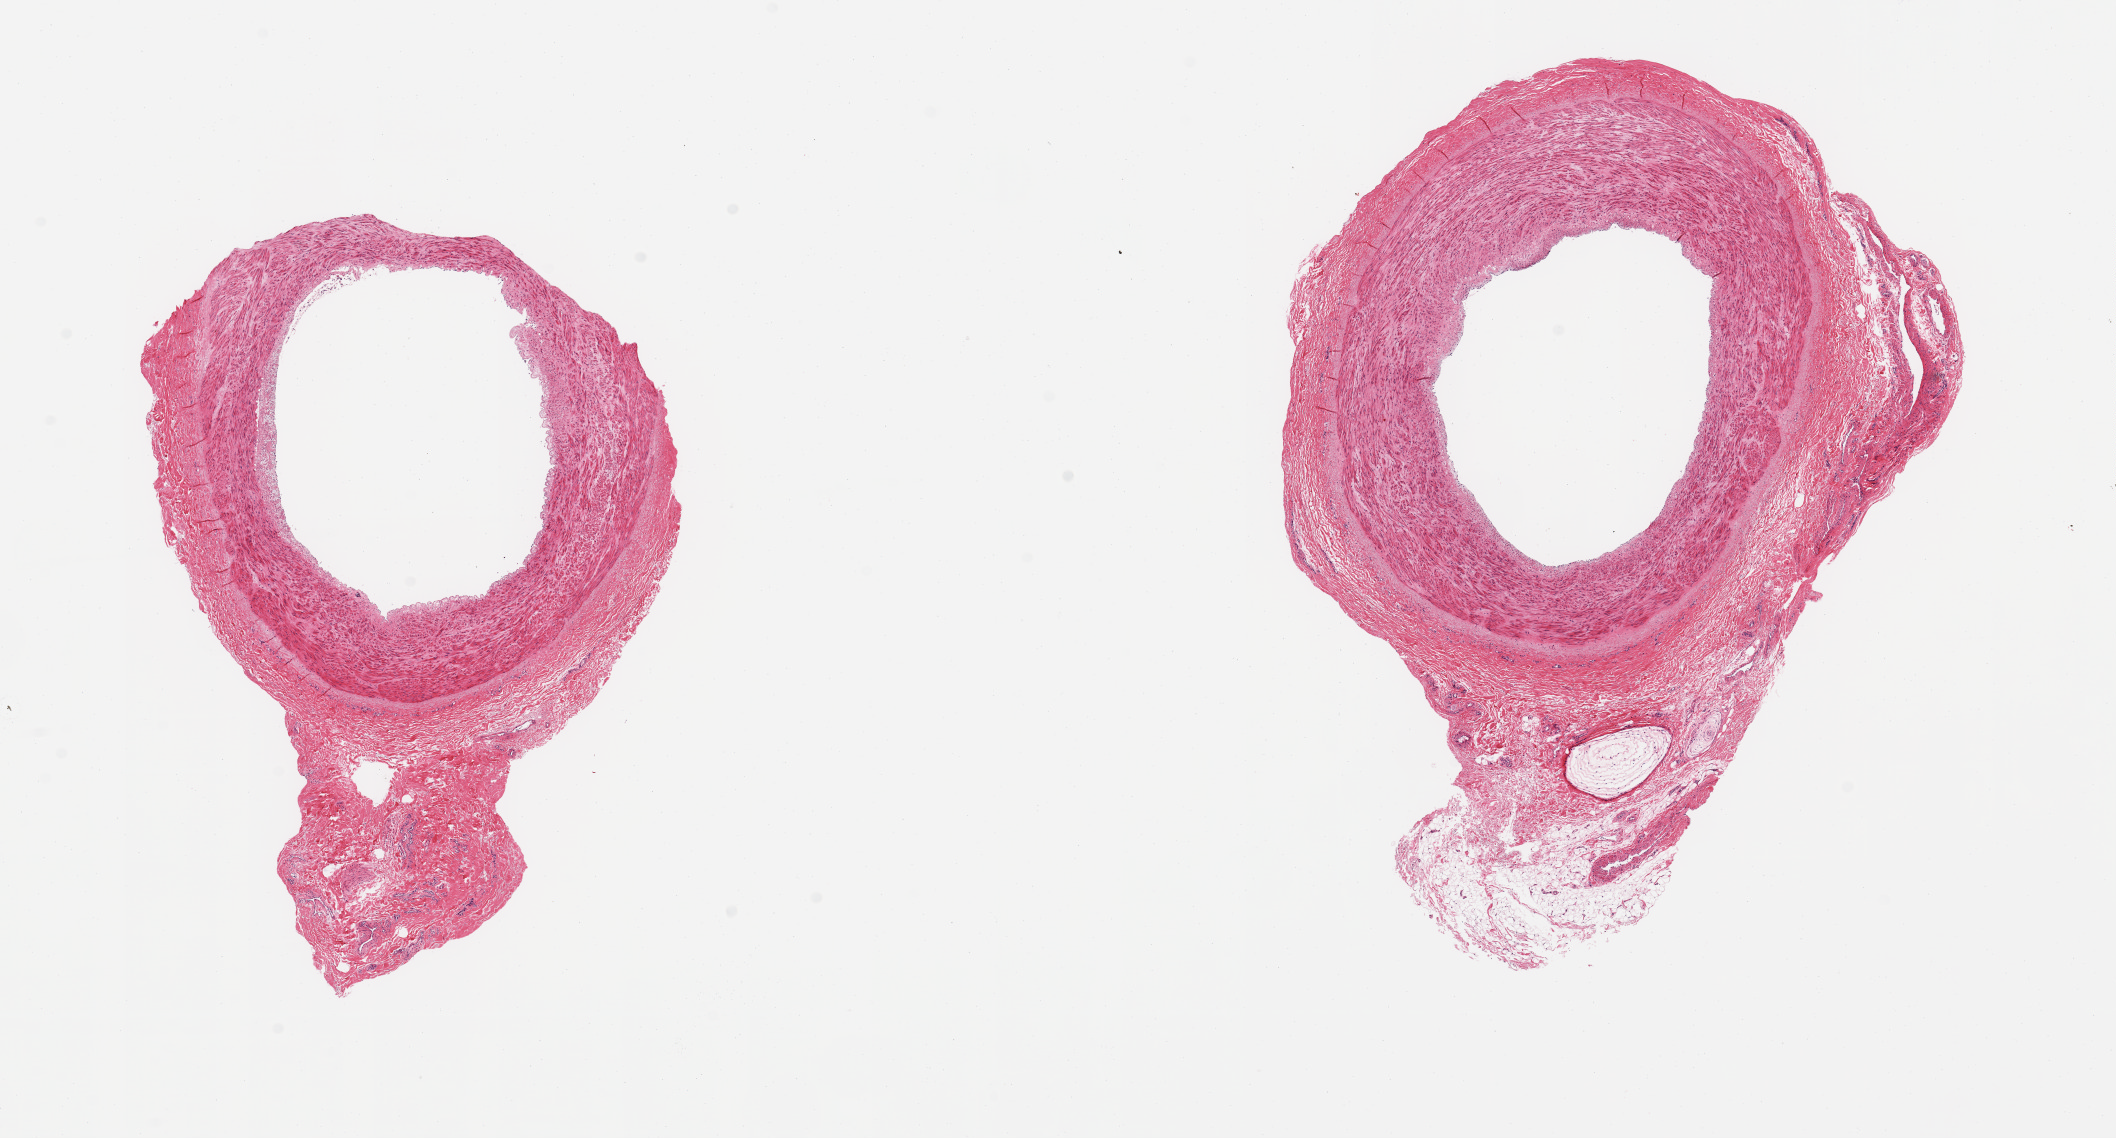
Haematoxylin and eosin whole-slide image, a low-resolution overview of the entire scanned area, about 16.7 x 9.0 mm (acquisition: 20x scan), PAXgene-fixed, paraffin-embedded tissue, target tissue: tibial artery, donor tissue sample. Male donor.
Reviewer comment on this tissue sample: 2 pieces; focal intimal thickening, include attachment of fat/fibroconnective tissue/pacinian corpuscle.